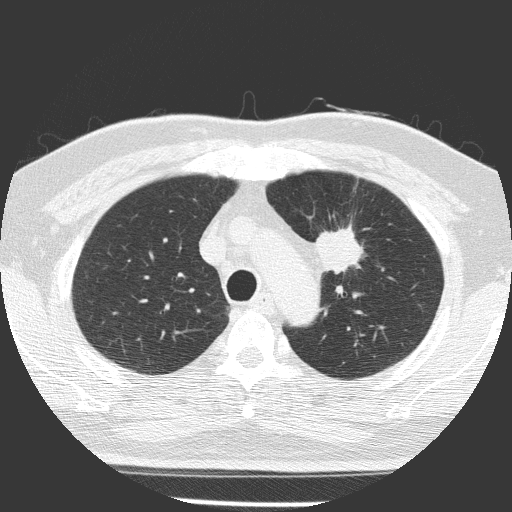
Low-dose screening chest CT, one axial slice; slice 116 of 156 in the series (ordered by position); 120 kVp; lung window (W 1500 / L -600 HU); 2 mm slice thickness; 512 × 512 image matrix, field of view 309 × 309 mm.
Outlined on this slice (expert manual segmentation):
- lesion 1 (tumor, upper lobe of left lung): bounding box [x1, y1, x2, y2] px = [315, 227, 363, 274]